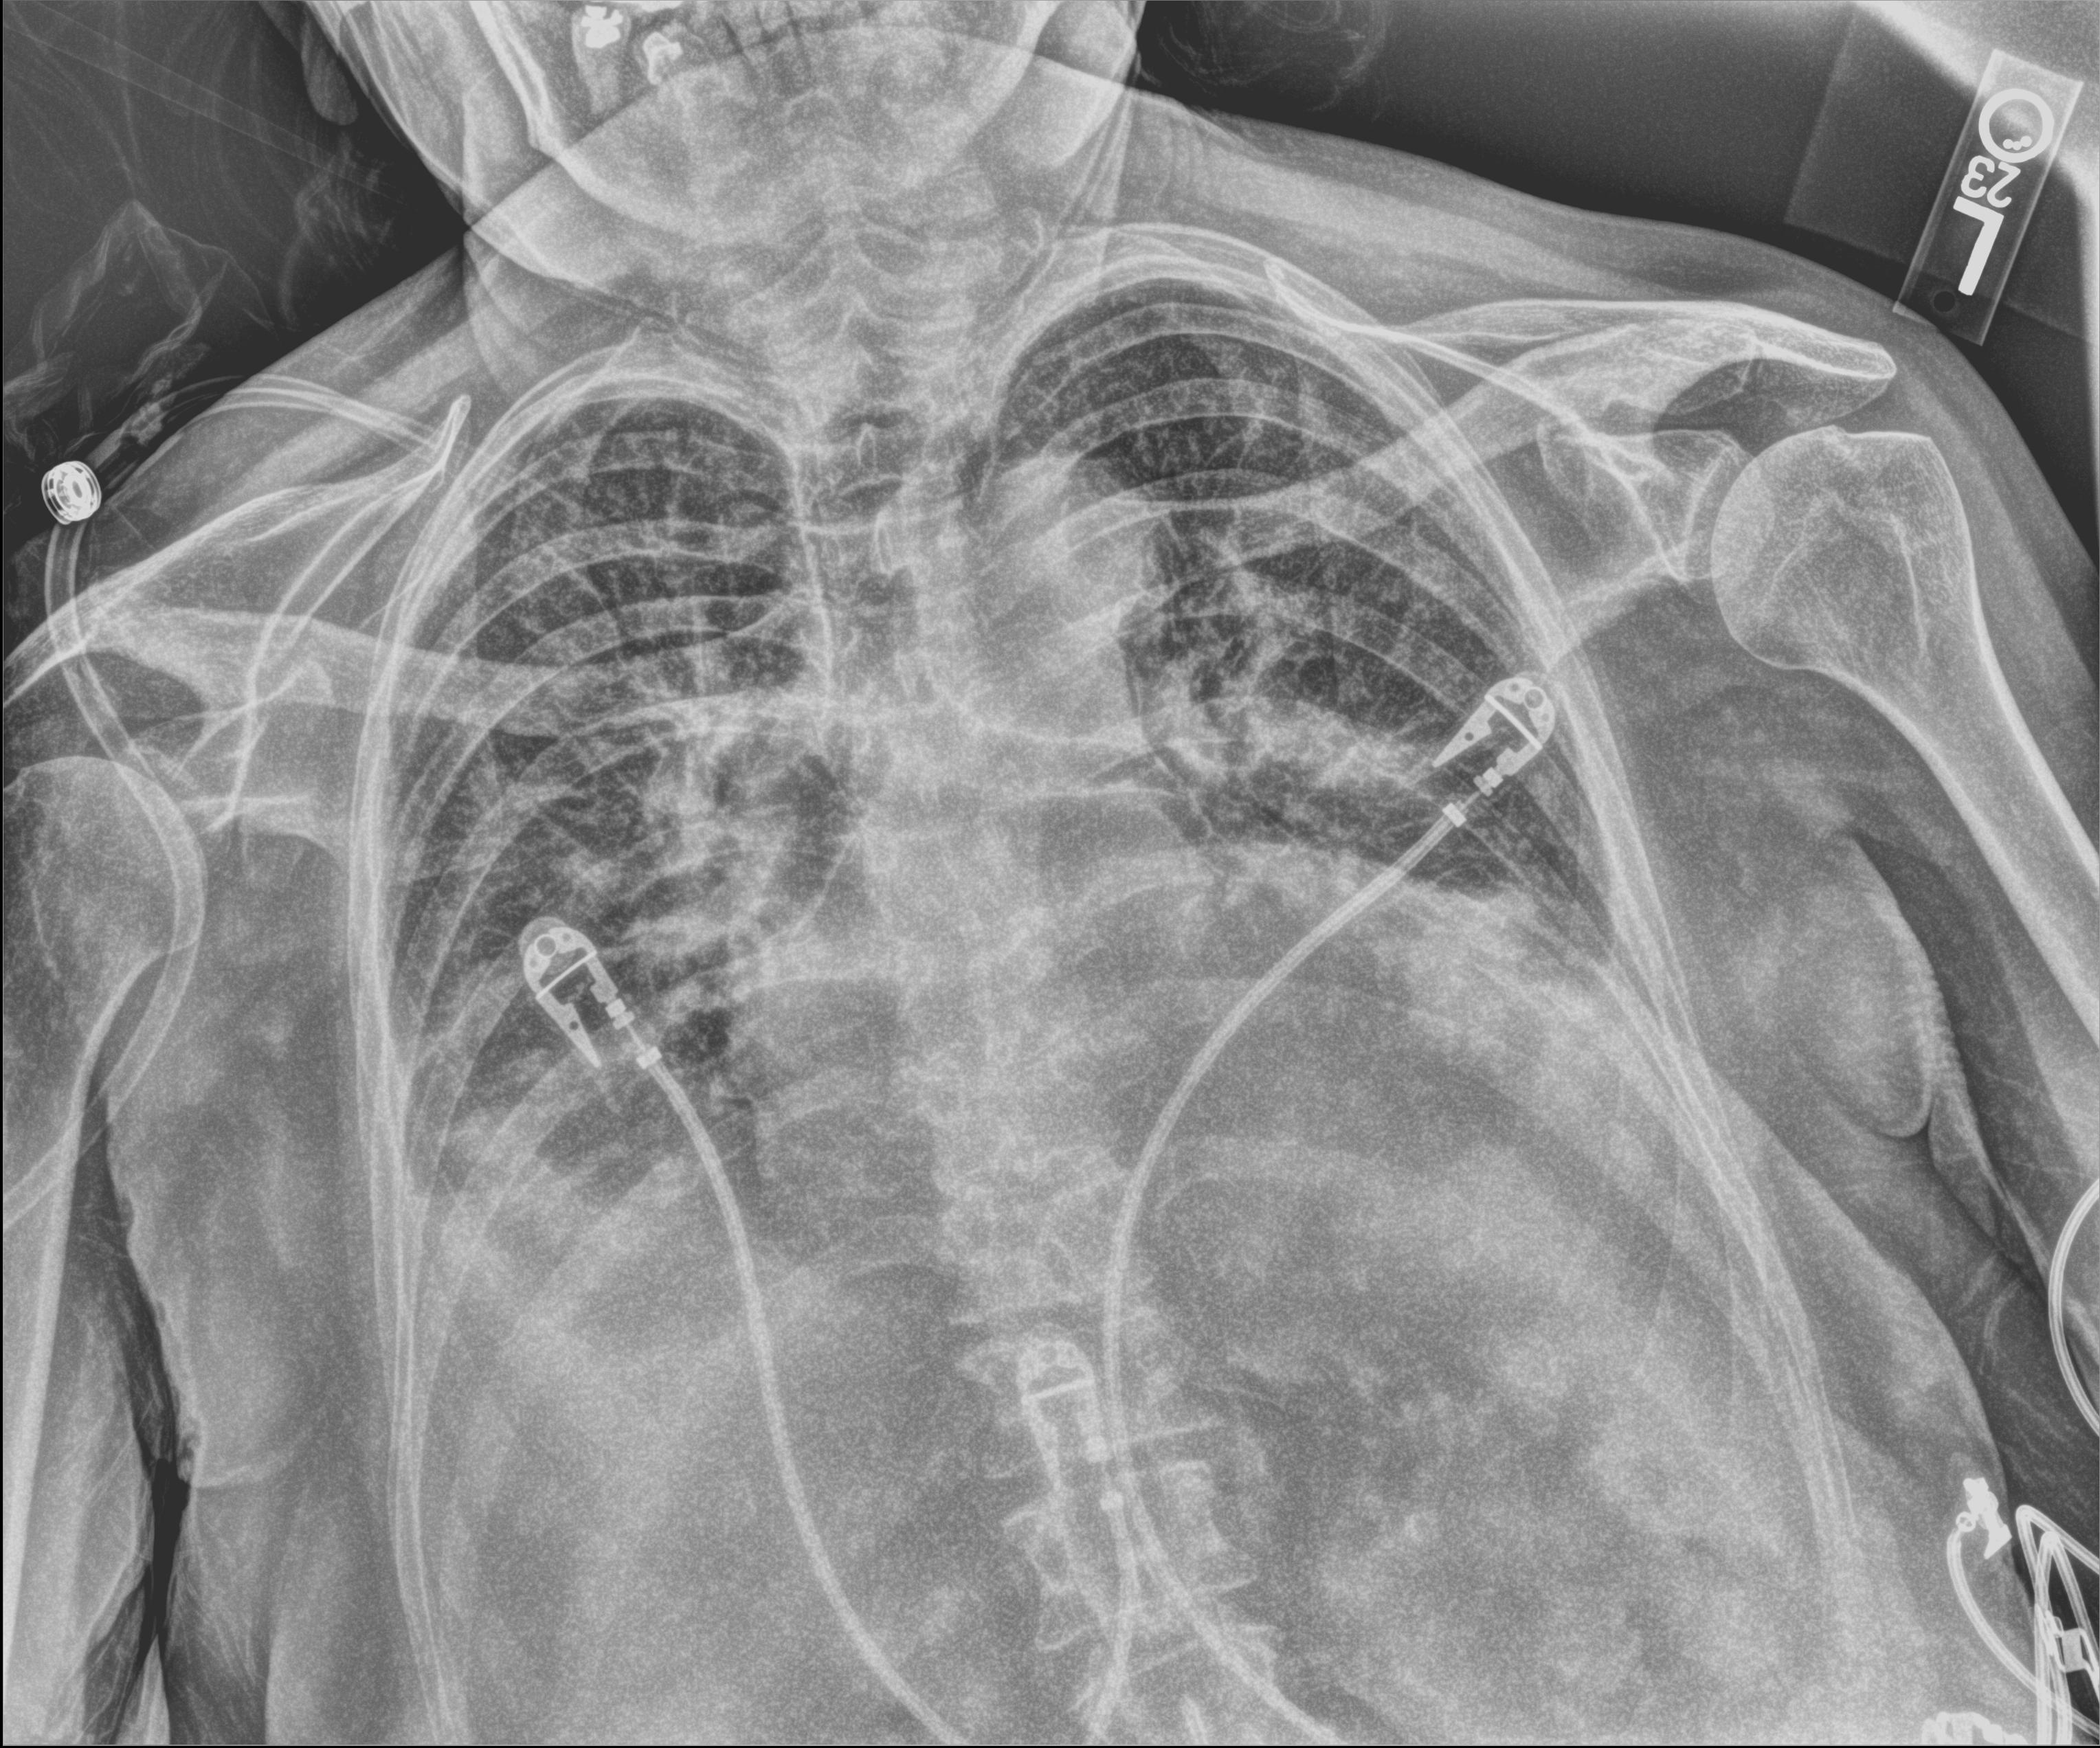
Portable chest radiograph; anteroposterior (AP) projection. Female patient hospitalised with COVID-19, age 75–90 years.
Hospital-stay facts (about this admission, not read from this image; timing relative to this image not recorded): admitted to intensive care during this hospital stay: no.